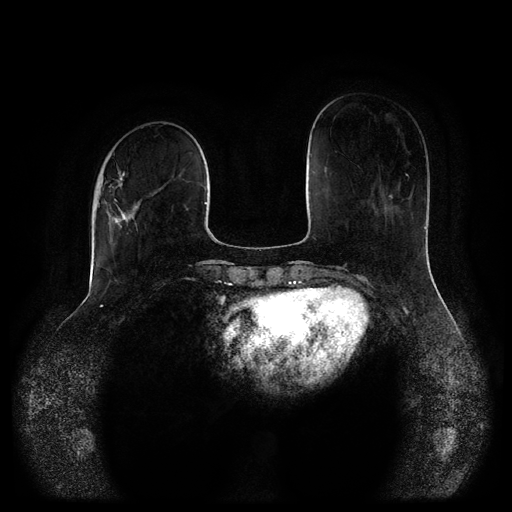
Breast MRI (dynamic contrast-enhanced, multi-phase), one axial slice. Position 31 of 116 along the scan axis. Dynamic contrast-enhanced series, time point 2 of 5 at this slice position (early post-contrast). 1.5 T. TE 2.6 ms, TR 5.2 ms. 2 mm slice thickness. 512 × 512 image matrix, field of view 380 × 380 mm. Female patient, age 52 years.
Structures marked on this image (semi-automatically segmented with operator editing):
- breast lesion (labelled 'tumour' in the annotation; benign lesions carry a separate 'benign' label): box from (x=103, y=171) to (x=142, y=245) px